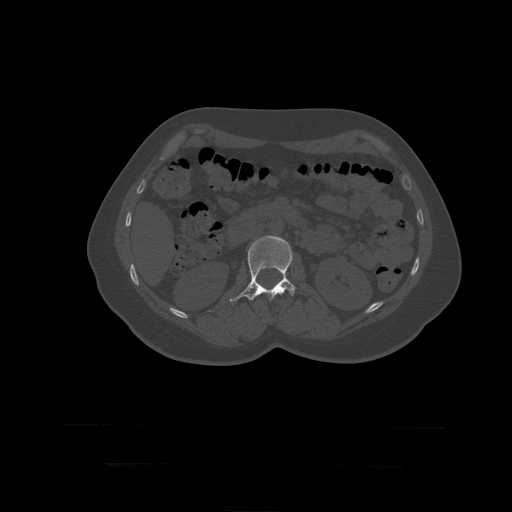
CT including the spine, one axial slice. Position 150 of 399 along the scan axis. Reconstruction kernel STANDARD. 120 kVp. Bone window (W 1800 / L 400 HU). 1.25 mm slice thickness. 512 × 512 image matrix, field of view 450 × 450 mm. Patient age 41 years. Case-level facts recorded for this patient, not image findings: primary cancer: breast.
Outlined on this slice (semi-automatically segmented with operator editing):
- L2 vertebra: bounding box <230,236,296,302> (left, top, right, bottom; pixels)